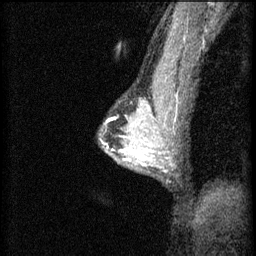
Breast MRI (dynamic contrast-enhanced), one sagittal slice. Slice 43 of 60 in the series (ordered by position). 3 images stored at this slice position (order not interpretable as contrast timing). 1.5 T. TE 4.2 ms, TR 8.2 ms. 256 × 256 image matrix. Patient: female, 44 years.
Annotated regions visible in this slice (semi-automatically segmented with operator editing):
- analysis volume of interest (the breast-tissue region the enhancement analysis was run in; not a lesion): bounding box (x1, y1, x2, y2) in pixels: (108, 132, 151, 159)
- tumour enhancement mask (voxels above the 70 % enhancement threshold inside the analysis volume of interest): (120, 136, 151, 159)